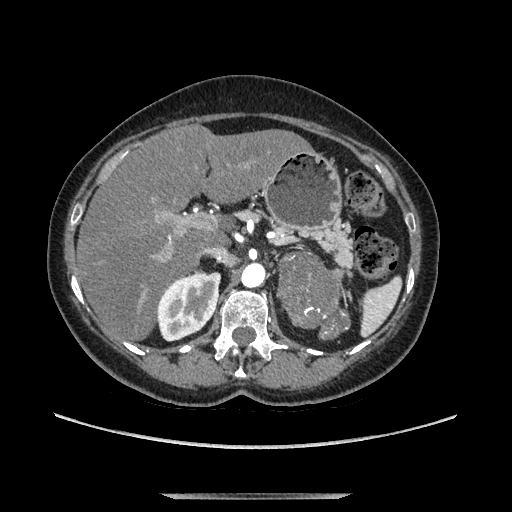
Contrast-enhanced abdominal CT, one axial slice. Slice 76 of 169 in the series (ordered by position). Soft-tissue window (W 400 / L 40 HU). 512 × 512 image matrix, field of view 400 × 400 mm. Female patient. Case-level facts recorded for this patient, not image findings: diagnosis: adrenocortical carcinoma; tumour side: left adrenal; tumour size at pathology: 9 cm; Ki-67 index: 2 %; stage (as recorded): 3.
Structures marked on this image (semi-automatic segmentation, software-assisted and operator-edited):
- mass: bounding box [x1, y1, x2, y2] px = [281, 252, 347, 338]